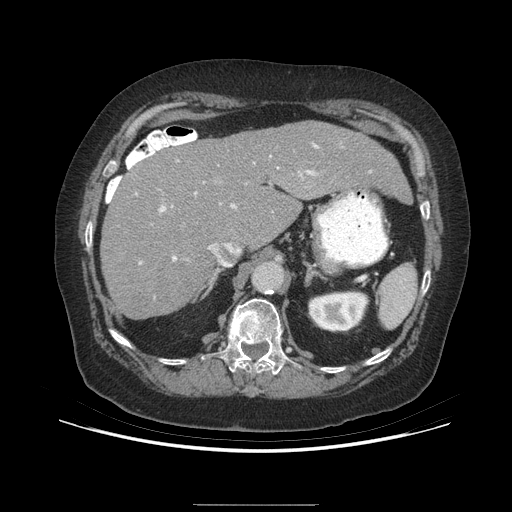
Contrast-enhanced abdominal CT (liver protocol), one axial slice; slice 161 of 192 in the series (ordered by position); reconstruction kernel STANDARD; soft-tissue window (W 400 / L 40 HU); 2.5 mm slice thickness; 512 × 512 image matrix. From the clinical record (not read from this slice): diagnosis: hepatocellular carcinoma (patient treated with transarterial chemoembolisation; whether this scan precedes or follows treatment is not stated here); TNM stage (as recorded): Stage-I; Child-Pugh class: A; tumour differentiation: moderately differentiated; tumour nodularity: uninodular.
Structures marked on this image (semi-automatically segmented with operator editing):
- liver parenchyma outside the tumour (the mass and vessels are separate outlines, so this box may not span the whole liver): box from (x=100, y=122) to (x=410, y=318) px
- liver vessels: (x=139, y=143)–(x=371, y=264)